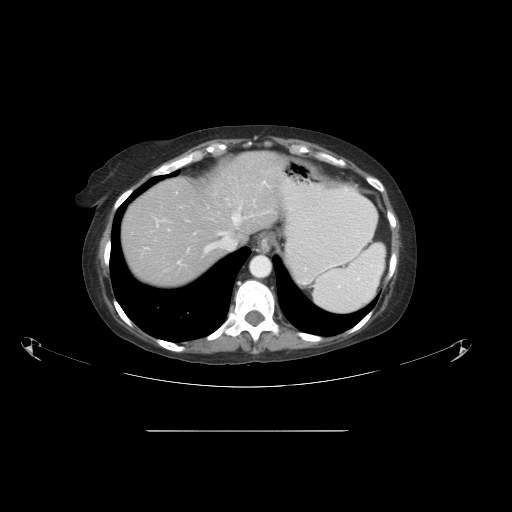
Contrast-enhanced abdominal CT, one axial slice. Slice 42 of 51 in the series (ordered by position). 120 kVp. Intravenous contrast given. Soft-tissue window (W 400 / L 40 HU). 5 mm slice thickness. 512 × 512 image matrix, field of view 475 × 475 mm. Female patient, age 48 years. From the clinical record (not read from this slice): diagnosis: colorectal cancer liver metastases, imaged before liver resection; multiple liver metastases: yes; largest metastasis: 1 cm; chemotherapy before resection: no.
Annotated regions visible in this slice (outlined manually by an expert reader):
- hepatic veins: bounding box [x1, y1, x2, y2] px = [205, 181, 268, 252]
- liver: [121, 153, 283, 287]
- planned liver remnant (the part of the liver to remain after resection): [121, 178, 232, 287]
- portal vein (with intrahepatic branches): [147, 220, 189, 264]